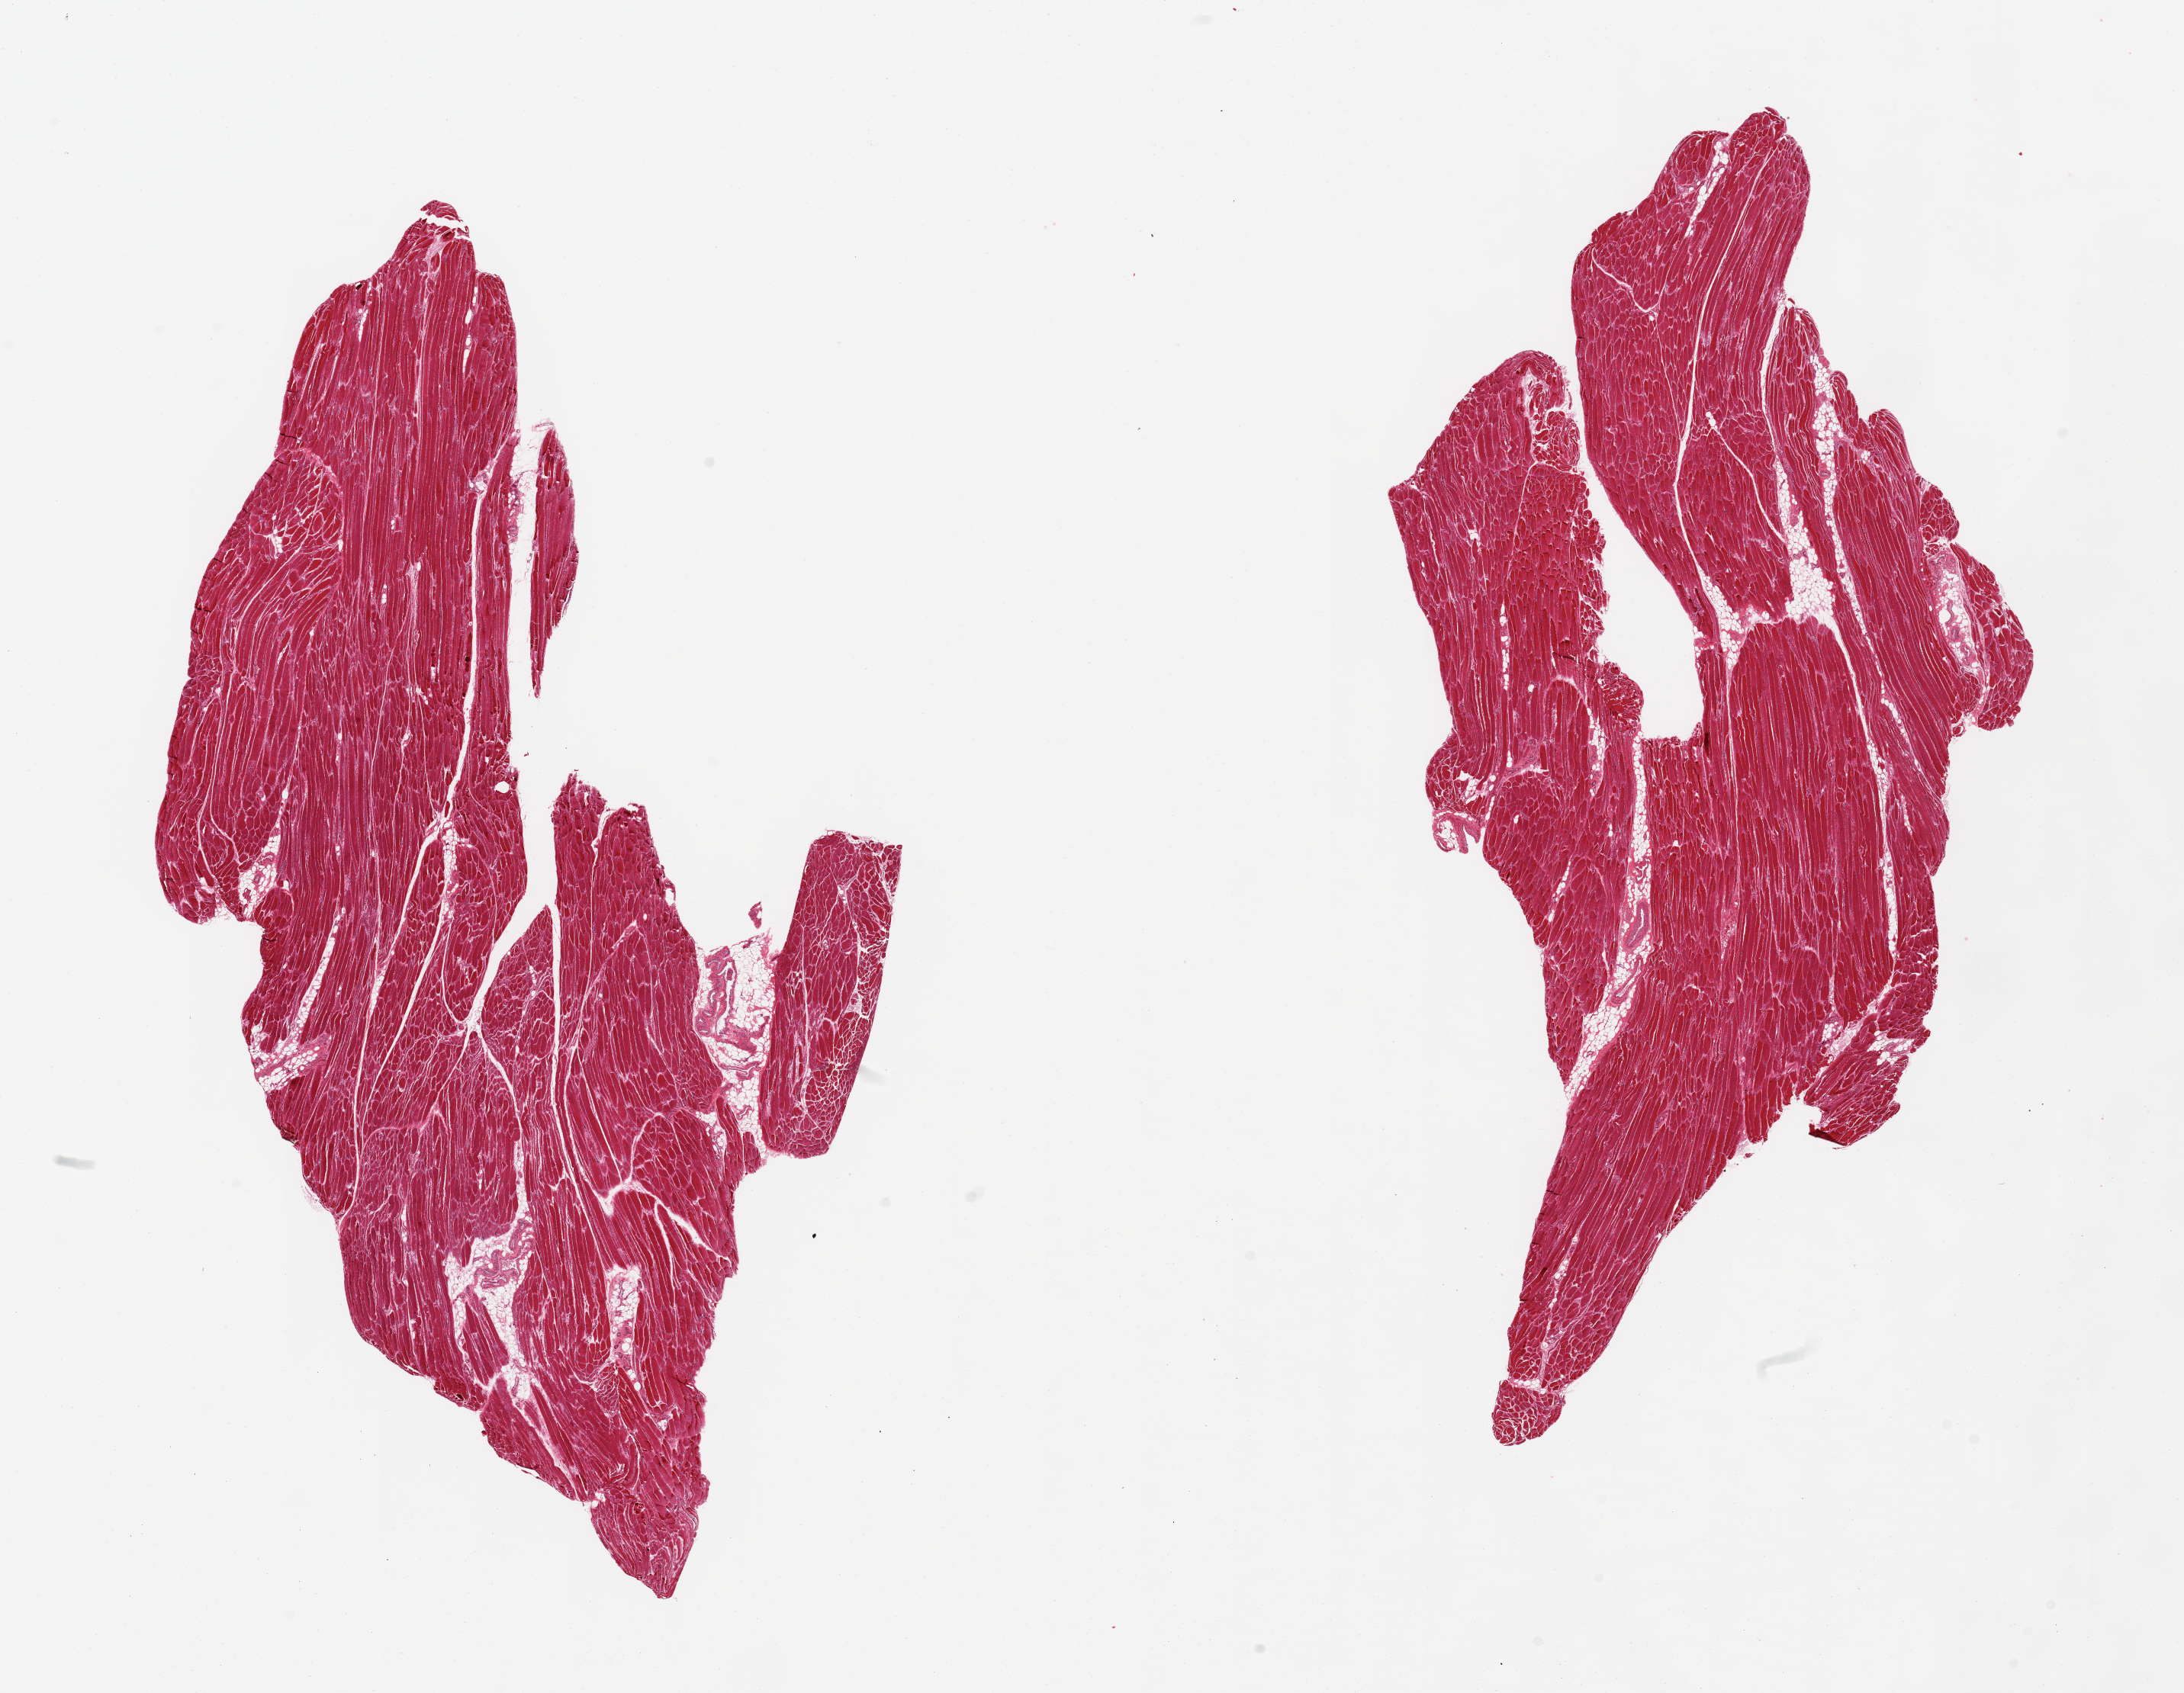
Digitized H&E-stained section, brightfield, shown as a low-resolution overview of the whole scanned area (about 22.6 x 17.6 mm, slide scanned at 20x), PAXgene-fixed, paraffin-embedded tissue, sampled site (target tissue): skeletal muscle, tissue donor sample. Male donor.
- reviewer comment on this tissue sample: 2 pieces, `10% interstitial fat